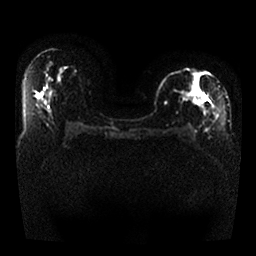
Breast MRI, one axial slice. Position 13 of 25 along the scan axis. Diffusion-weighted series; image 2 of 4 stored at this slice position (different b-values; order by instance number). 1.5 T. 4 mm slice thickness. 256 × 256 image matrix, field of view 330 × 330 mm. Female patient.
Structures marked on this image (manually delineated by an expert):
- tumour on diffusion-weighted imaging: bounding box (x1, y1, x2, y2) in pixels: (172, 89, 205, 112)